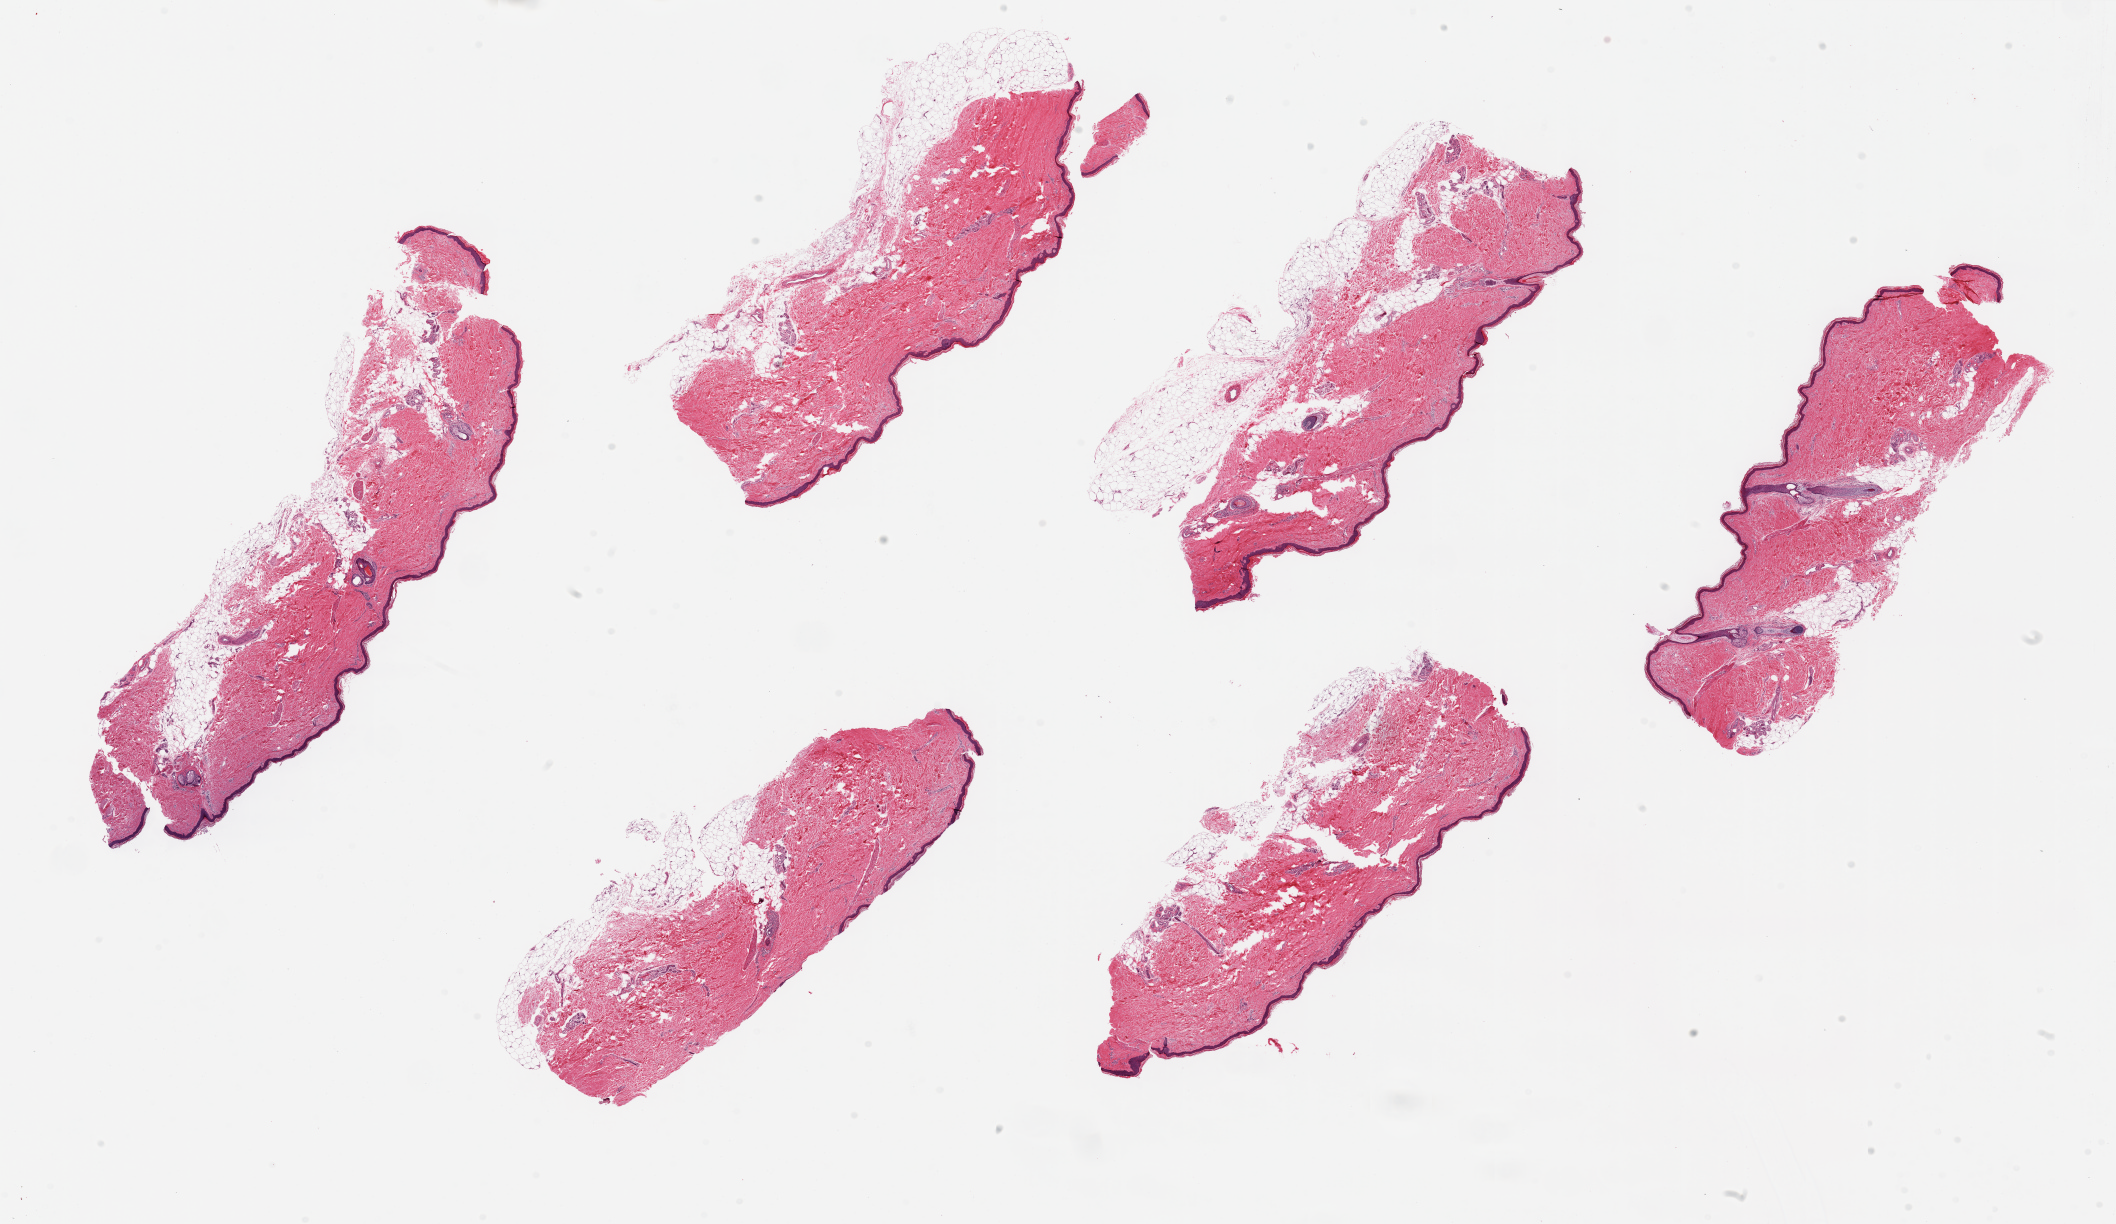
Whole-slide image, hematoxylin and eosin (H&E) stain, brightfield, low-resolution overview of the scanned area, about 33.5 x 19.4 mm, PAXgene-fixed, paraffin-embedded tissue, section of skin of lower leg (target tissue), tissue donor sample.
* reviewer comment on this tissue sample: 6 pieces ~7x2mm; Up to ~1mm layer of fat on dermal surface of several; Squamous mucosa is ~2-3% of thickness